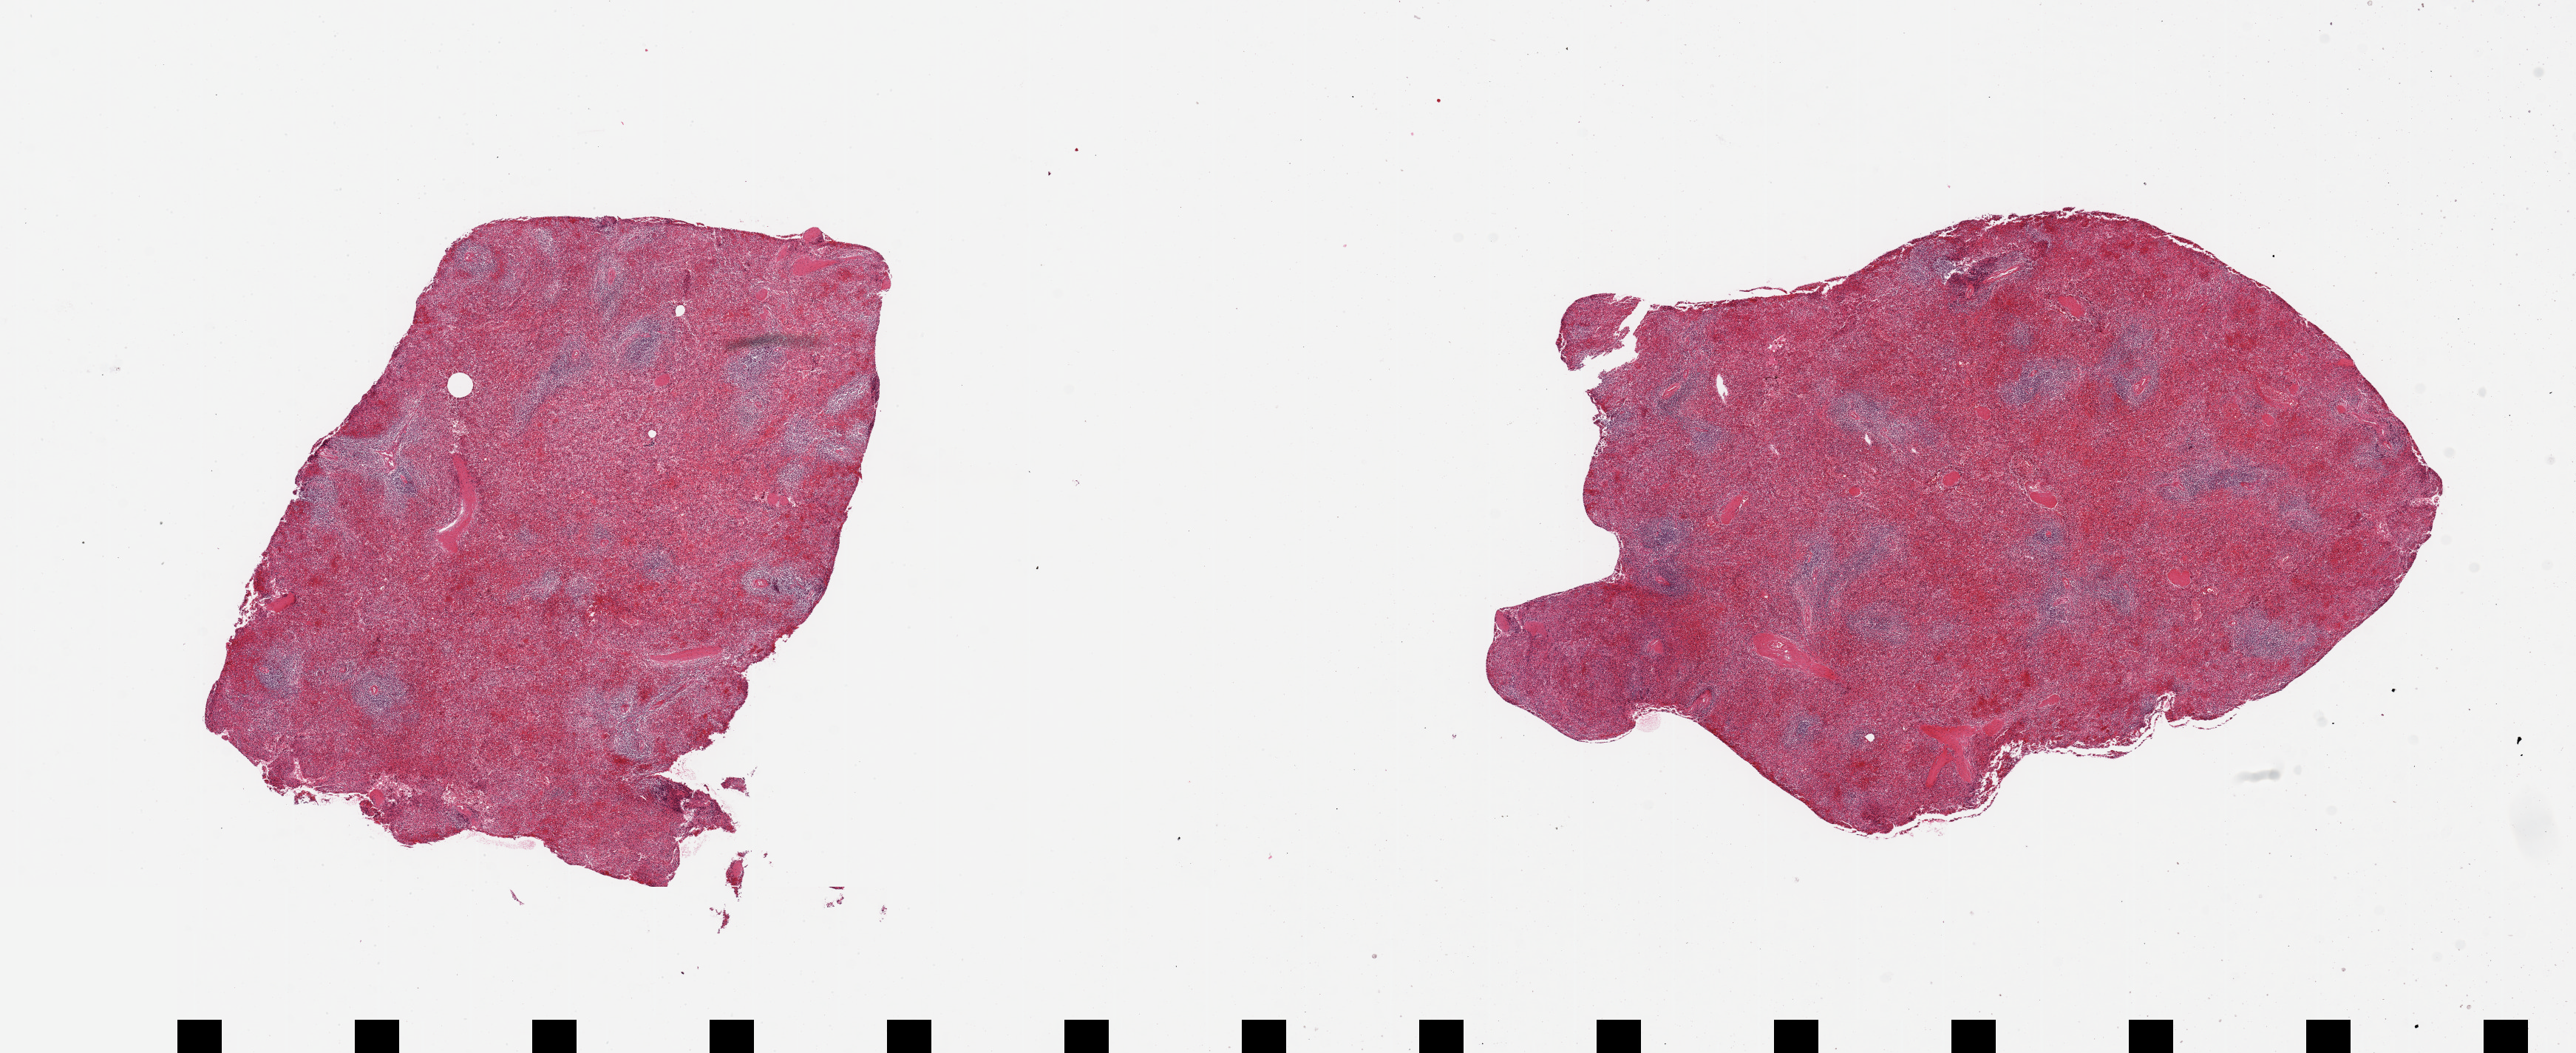
Haematoxylin and eosin whole-slide image — low-resolution overview of the scanned area, about 27.6 x 11.3 mm (slide scanned at 20x), PAXgene-fixed paraffin-embedded (PFPE) section, sampled site (target tissue): spleen, donor tissue sample.
Pathologist's review note for this sample: 2 pieces; no germinal centers seen.